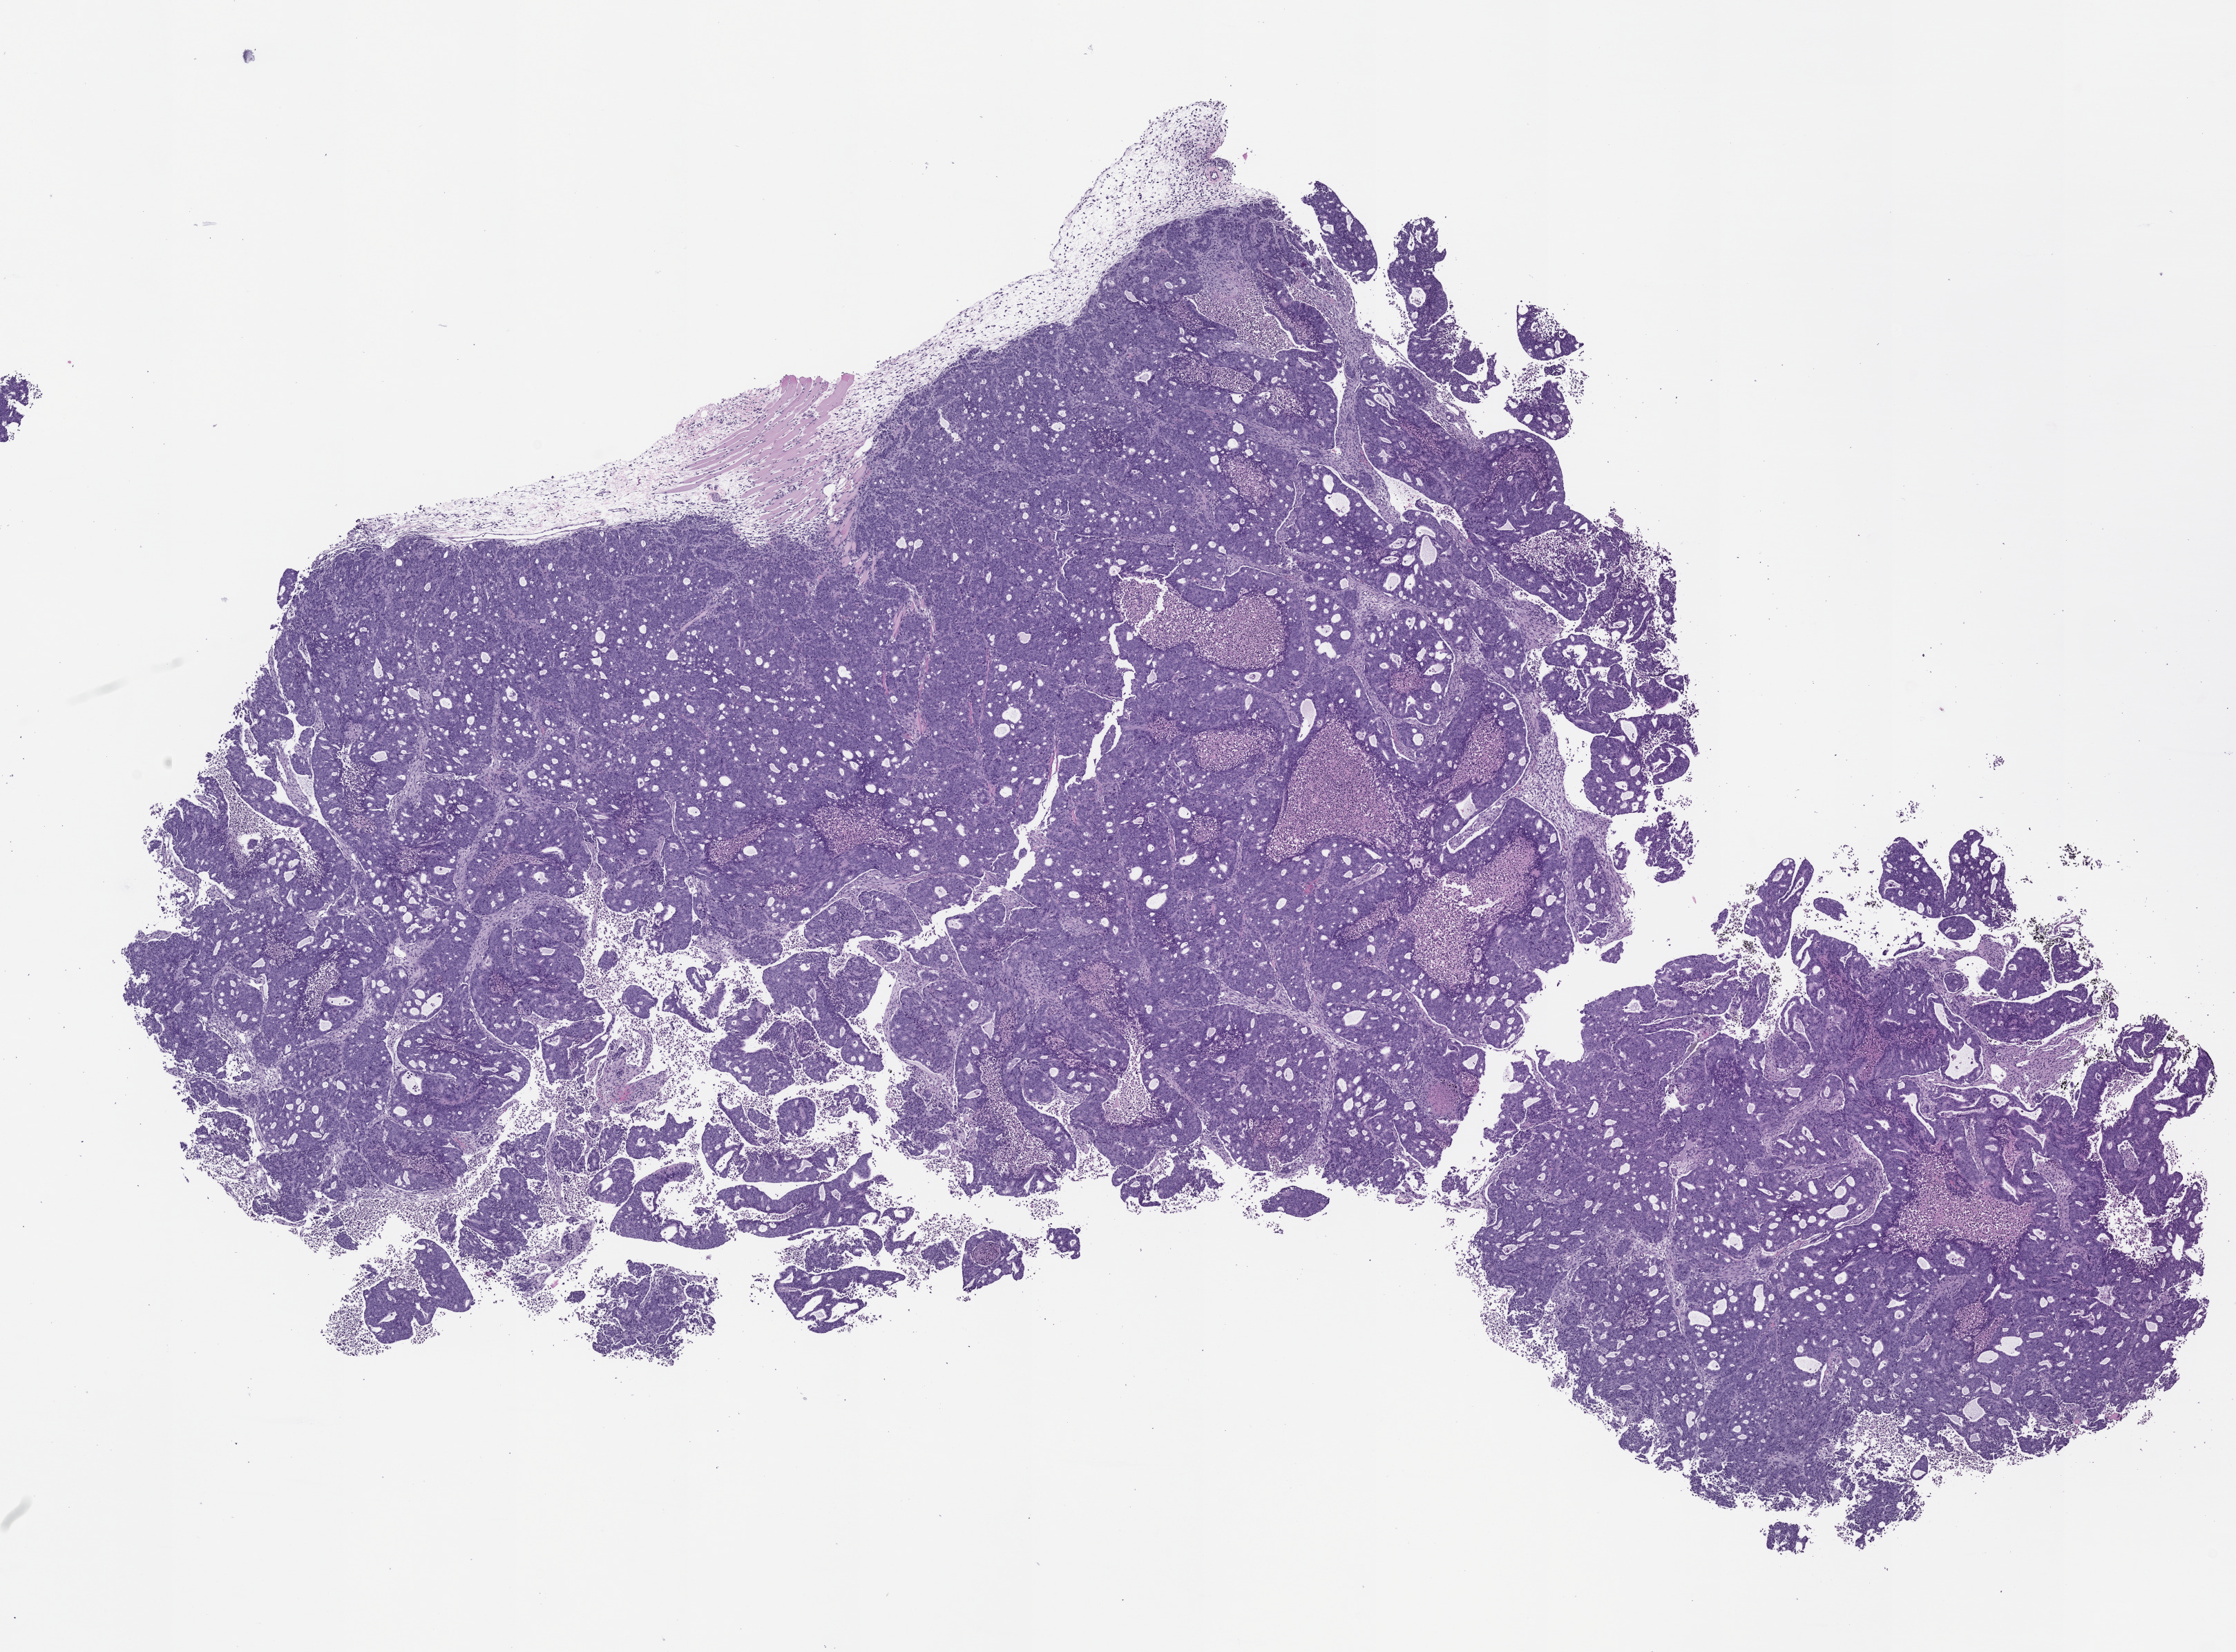
Haematoxylin and eosin whole-slide image of a patient-derived xenograft (PDX) tumor grown in a mouse, passage 1 — a low-resolution overview of the entire scanned area, about 13.0 x 9.6 mm. Formalin-fixed paraffin-embedded section. Originating tumor site category: colon.
Originating patient diagnosis: Colon Adenocarcinoma.